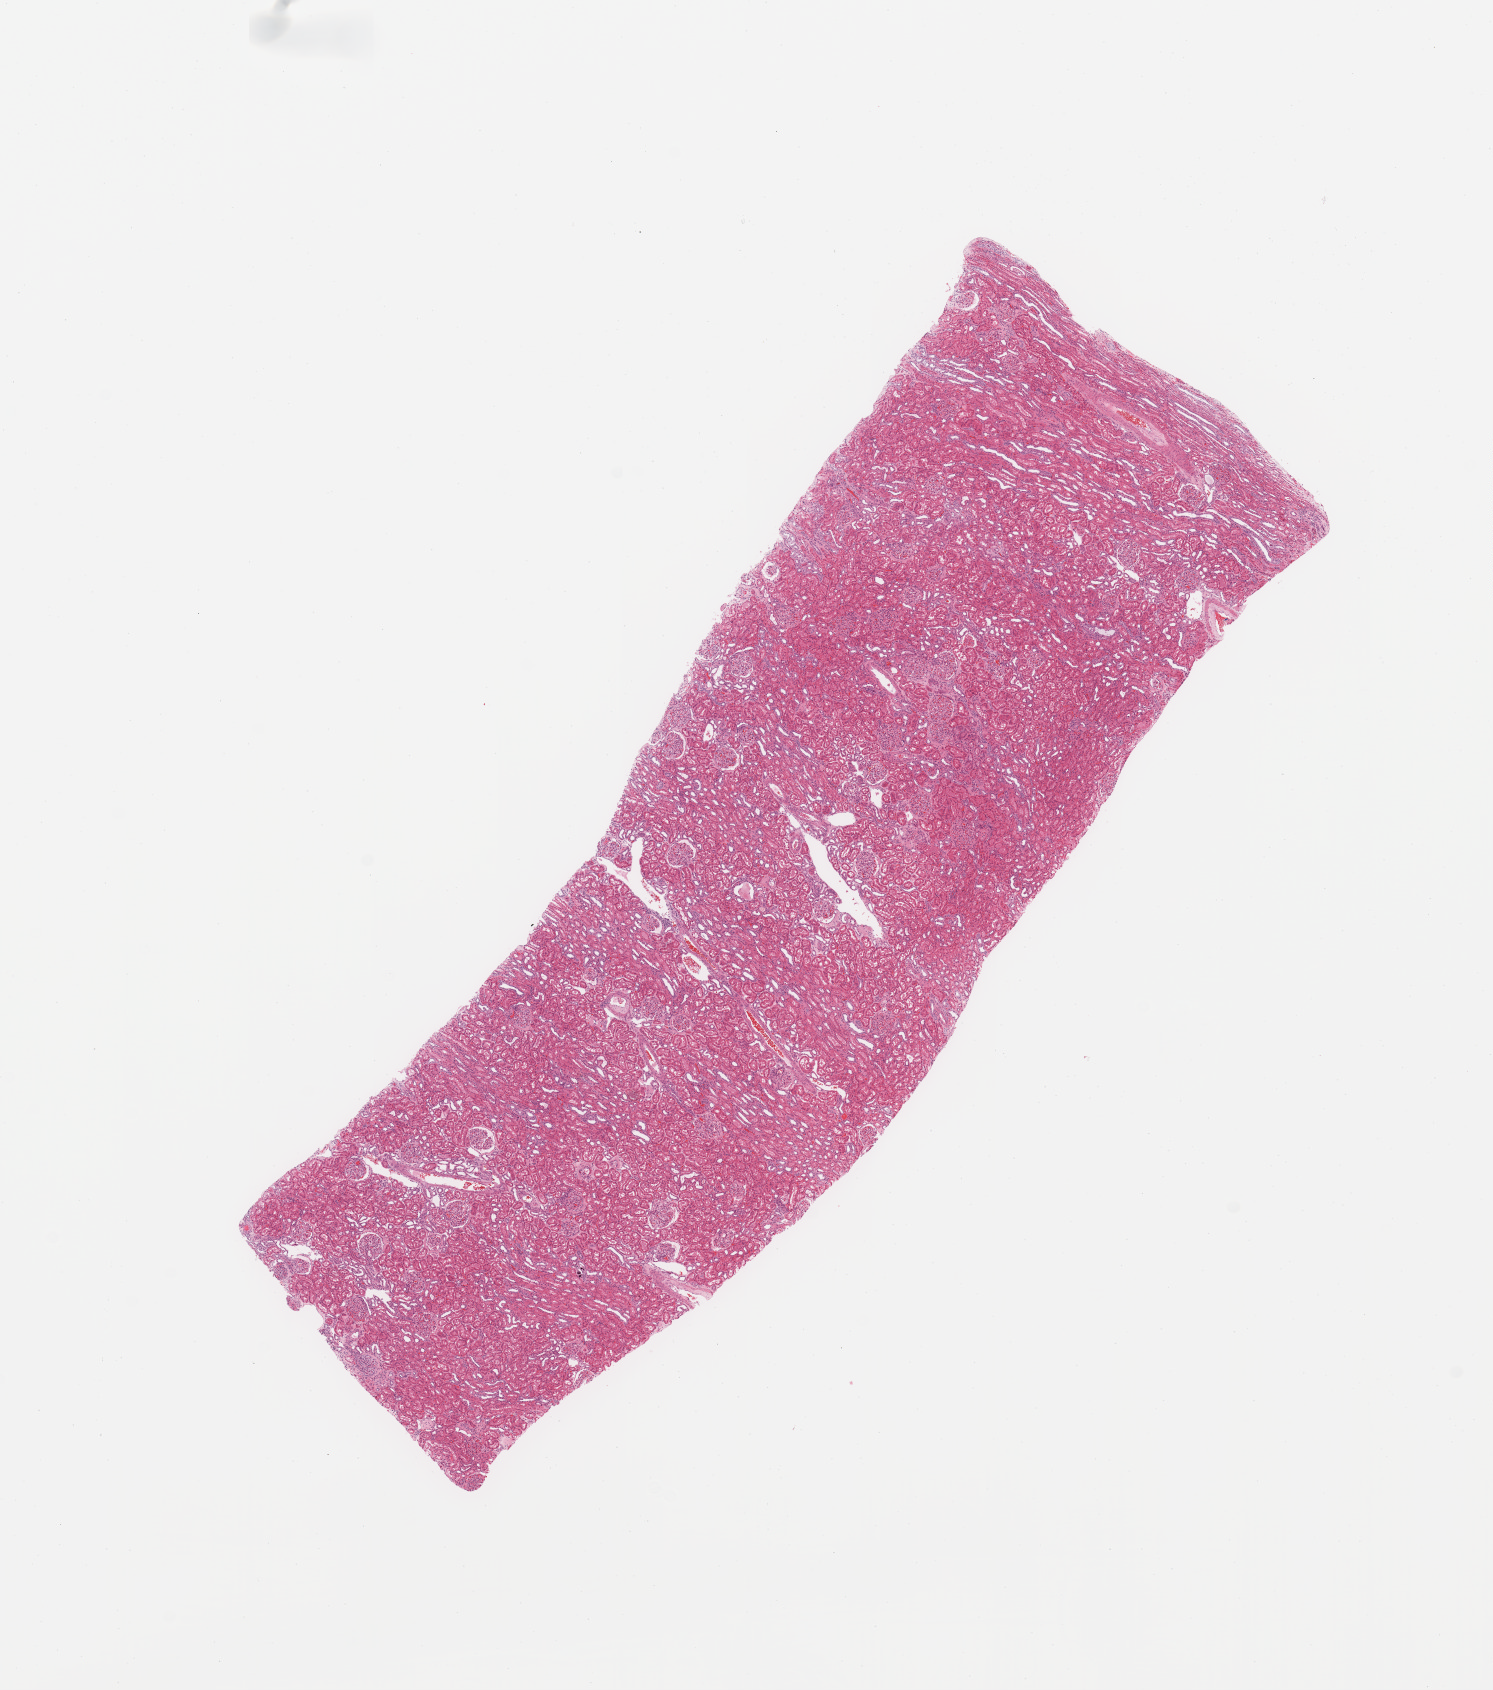
Digitized Hematoxylin and eosin (H&E) stained tissue section (whole slide), low-resolution overview of the scanned area, about 11.8 x 13.4 mm (slide scanned at 20x); normal (non-tumour) tissue sample, sampled site: kidney. Patient: male, age 35 years.
This section: normal (non-tumour) tissue from the same patient. Patient diagnosis: Renal cell carcinoma, NOS.